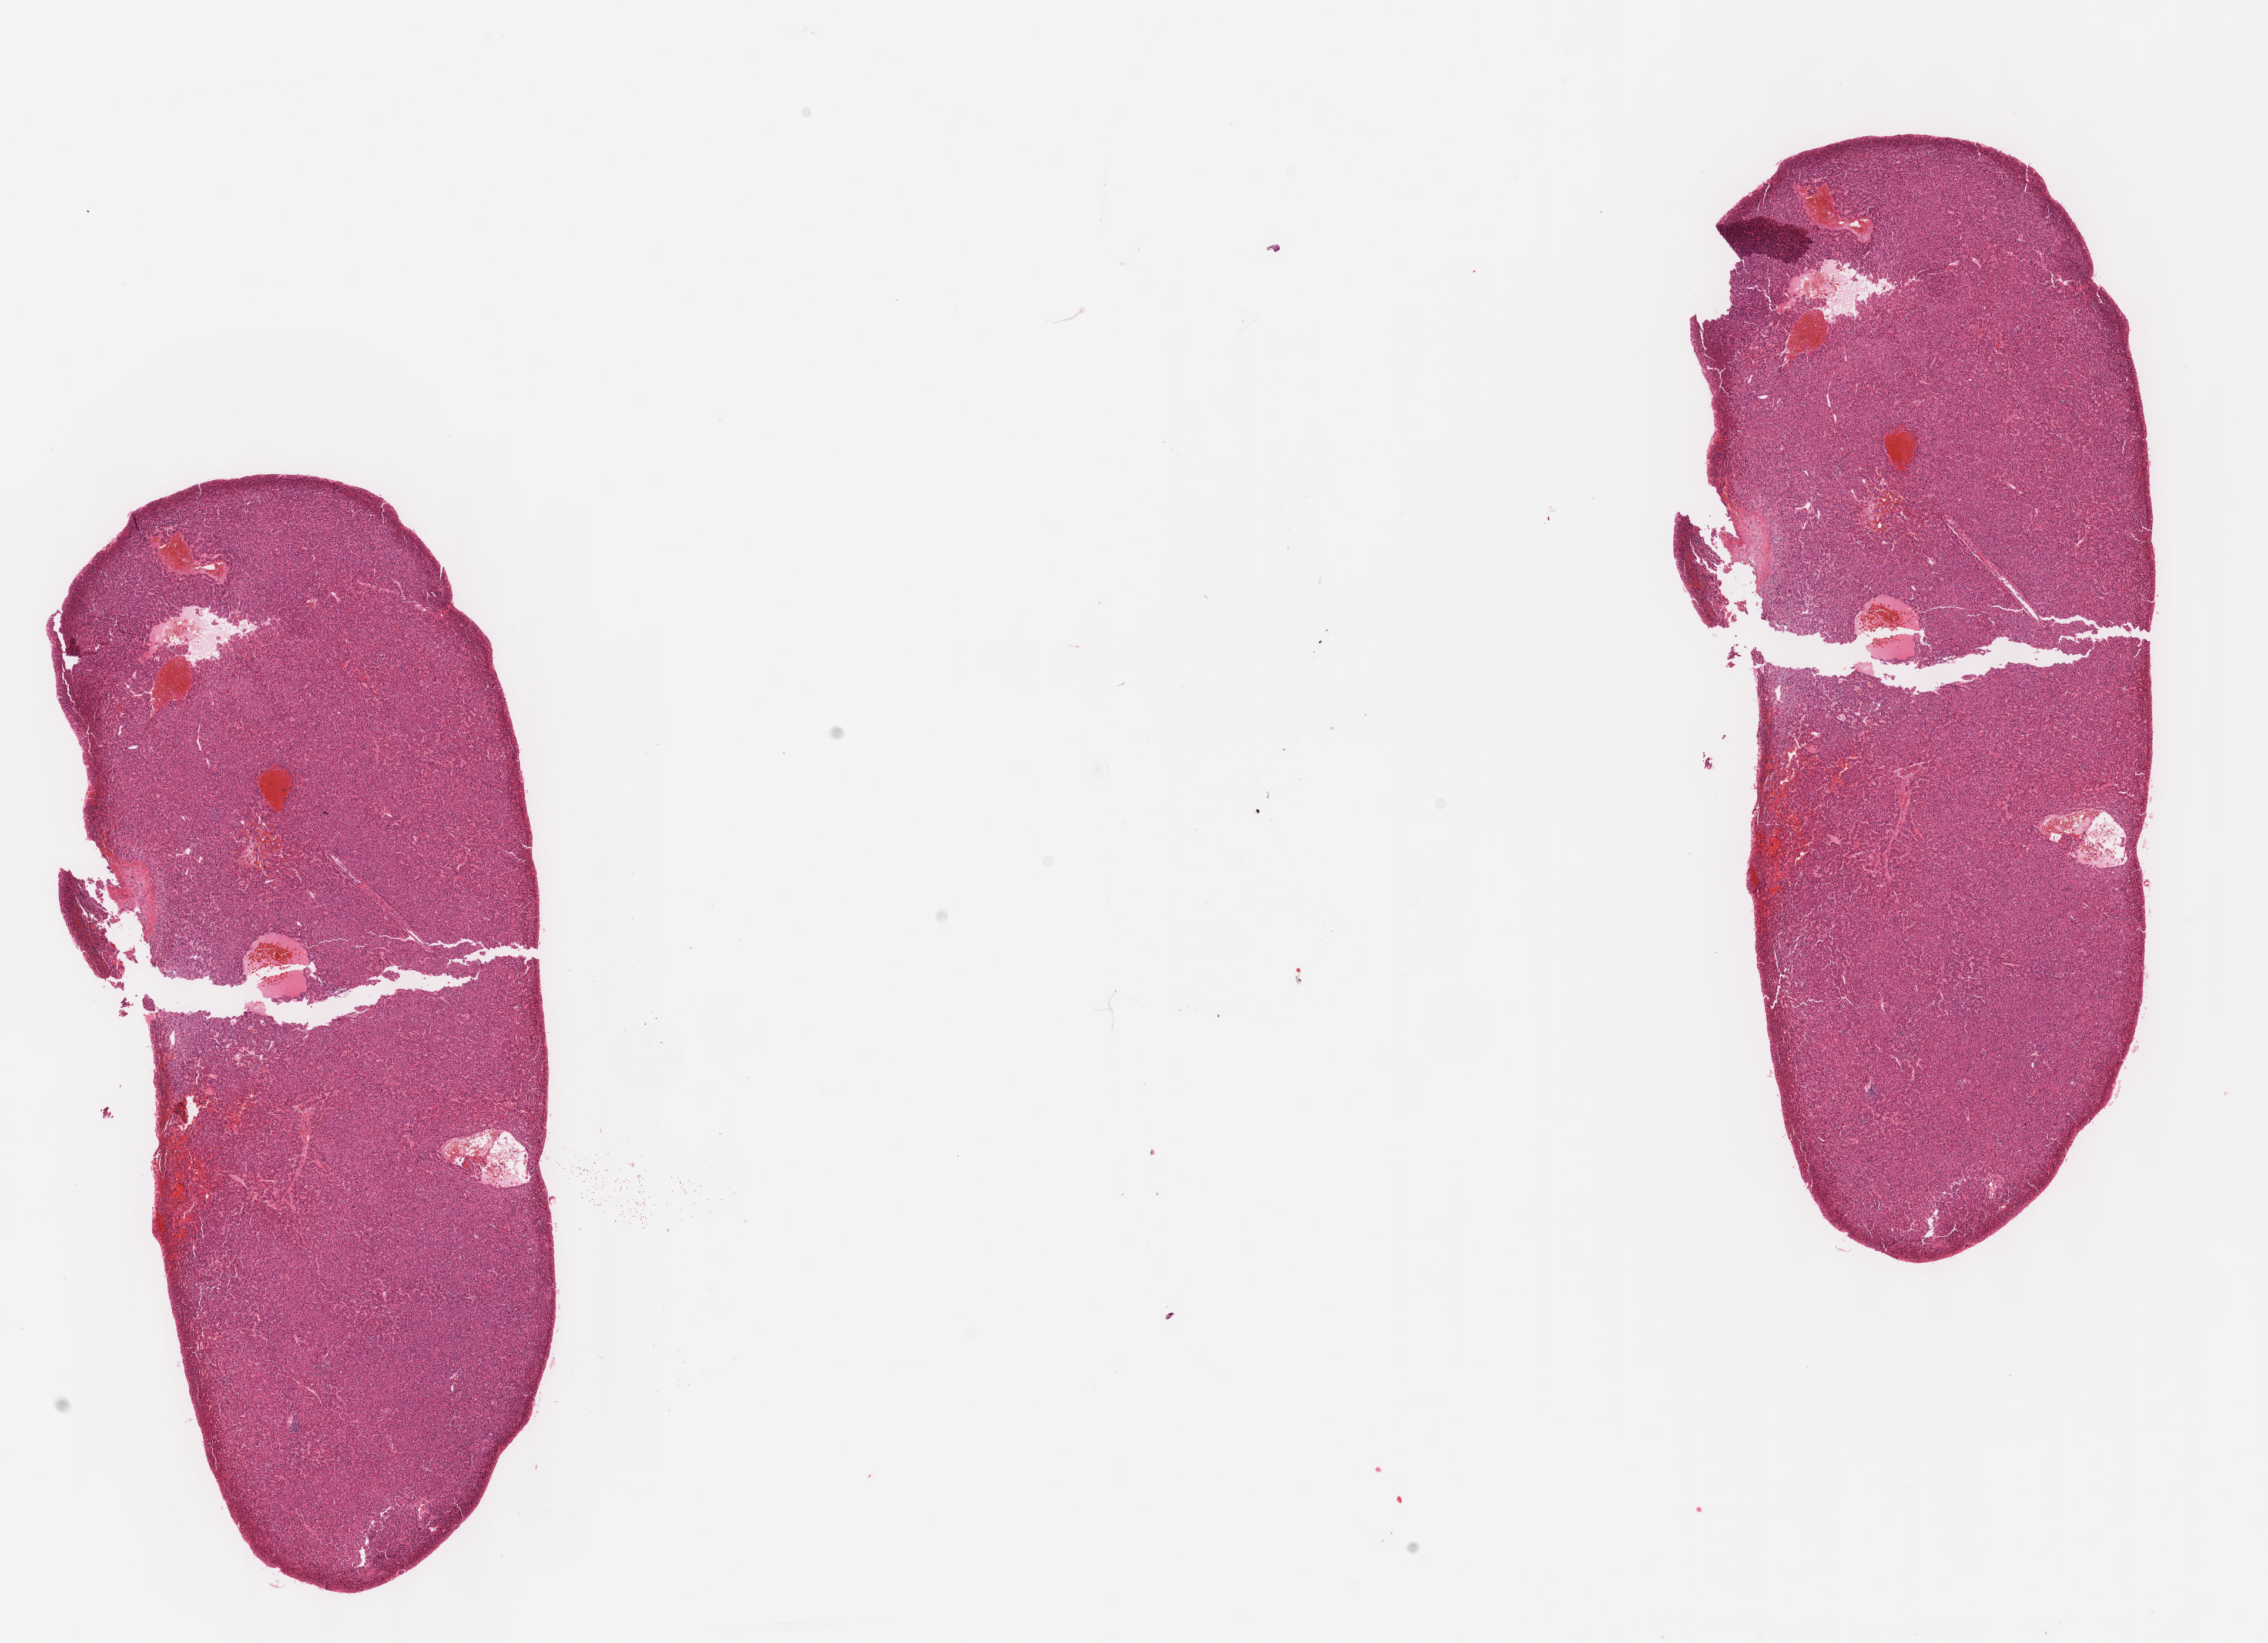
Digitized H&E-stained tissue section (whole slide) — shown as a low-resolution overview of the whole scanned area (about 15.6 x 11.3 mm, acquisition: 40x scan); formalin-fixed paraffin-embedded (FFPE) diagnostic section; liver, primary tumour sample. Female, age 49 years at initial diagnosis. Histologic grade: G1 (well differentiated).
Histologic diagnosis: Hepatocellular carcinoma, NOS. AJCC pathologic stage: I (7th edition). TNM: T1 N0 M0.